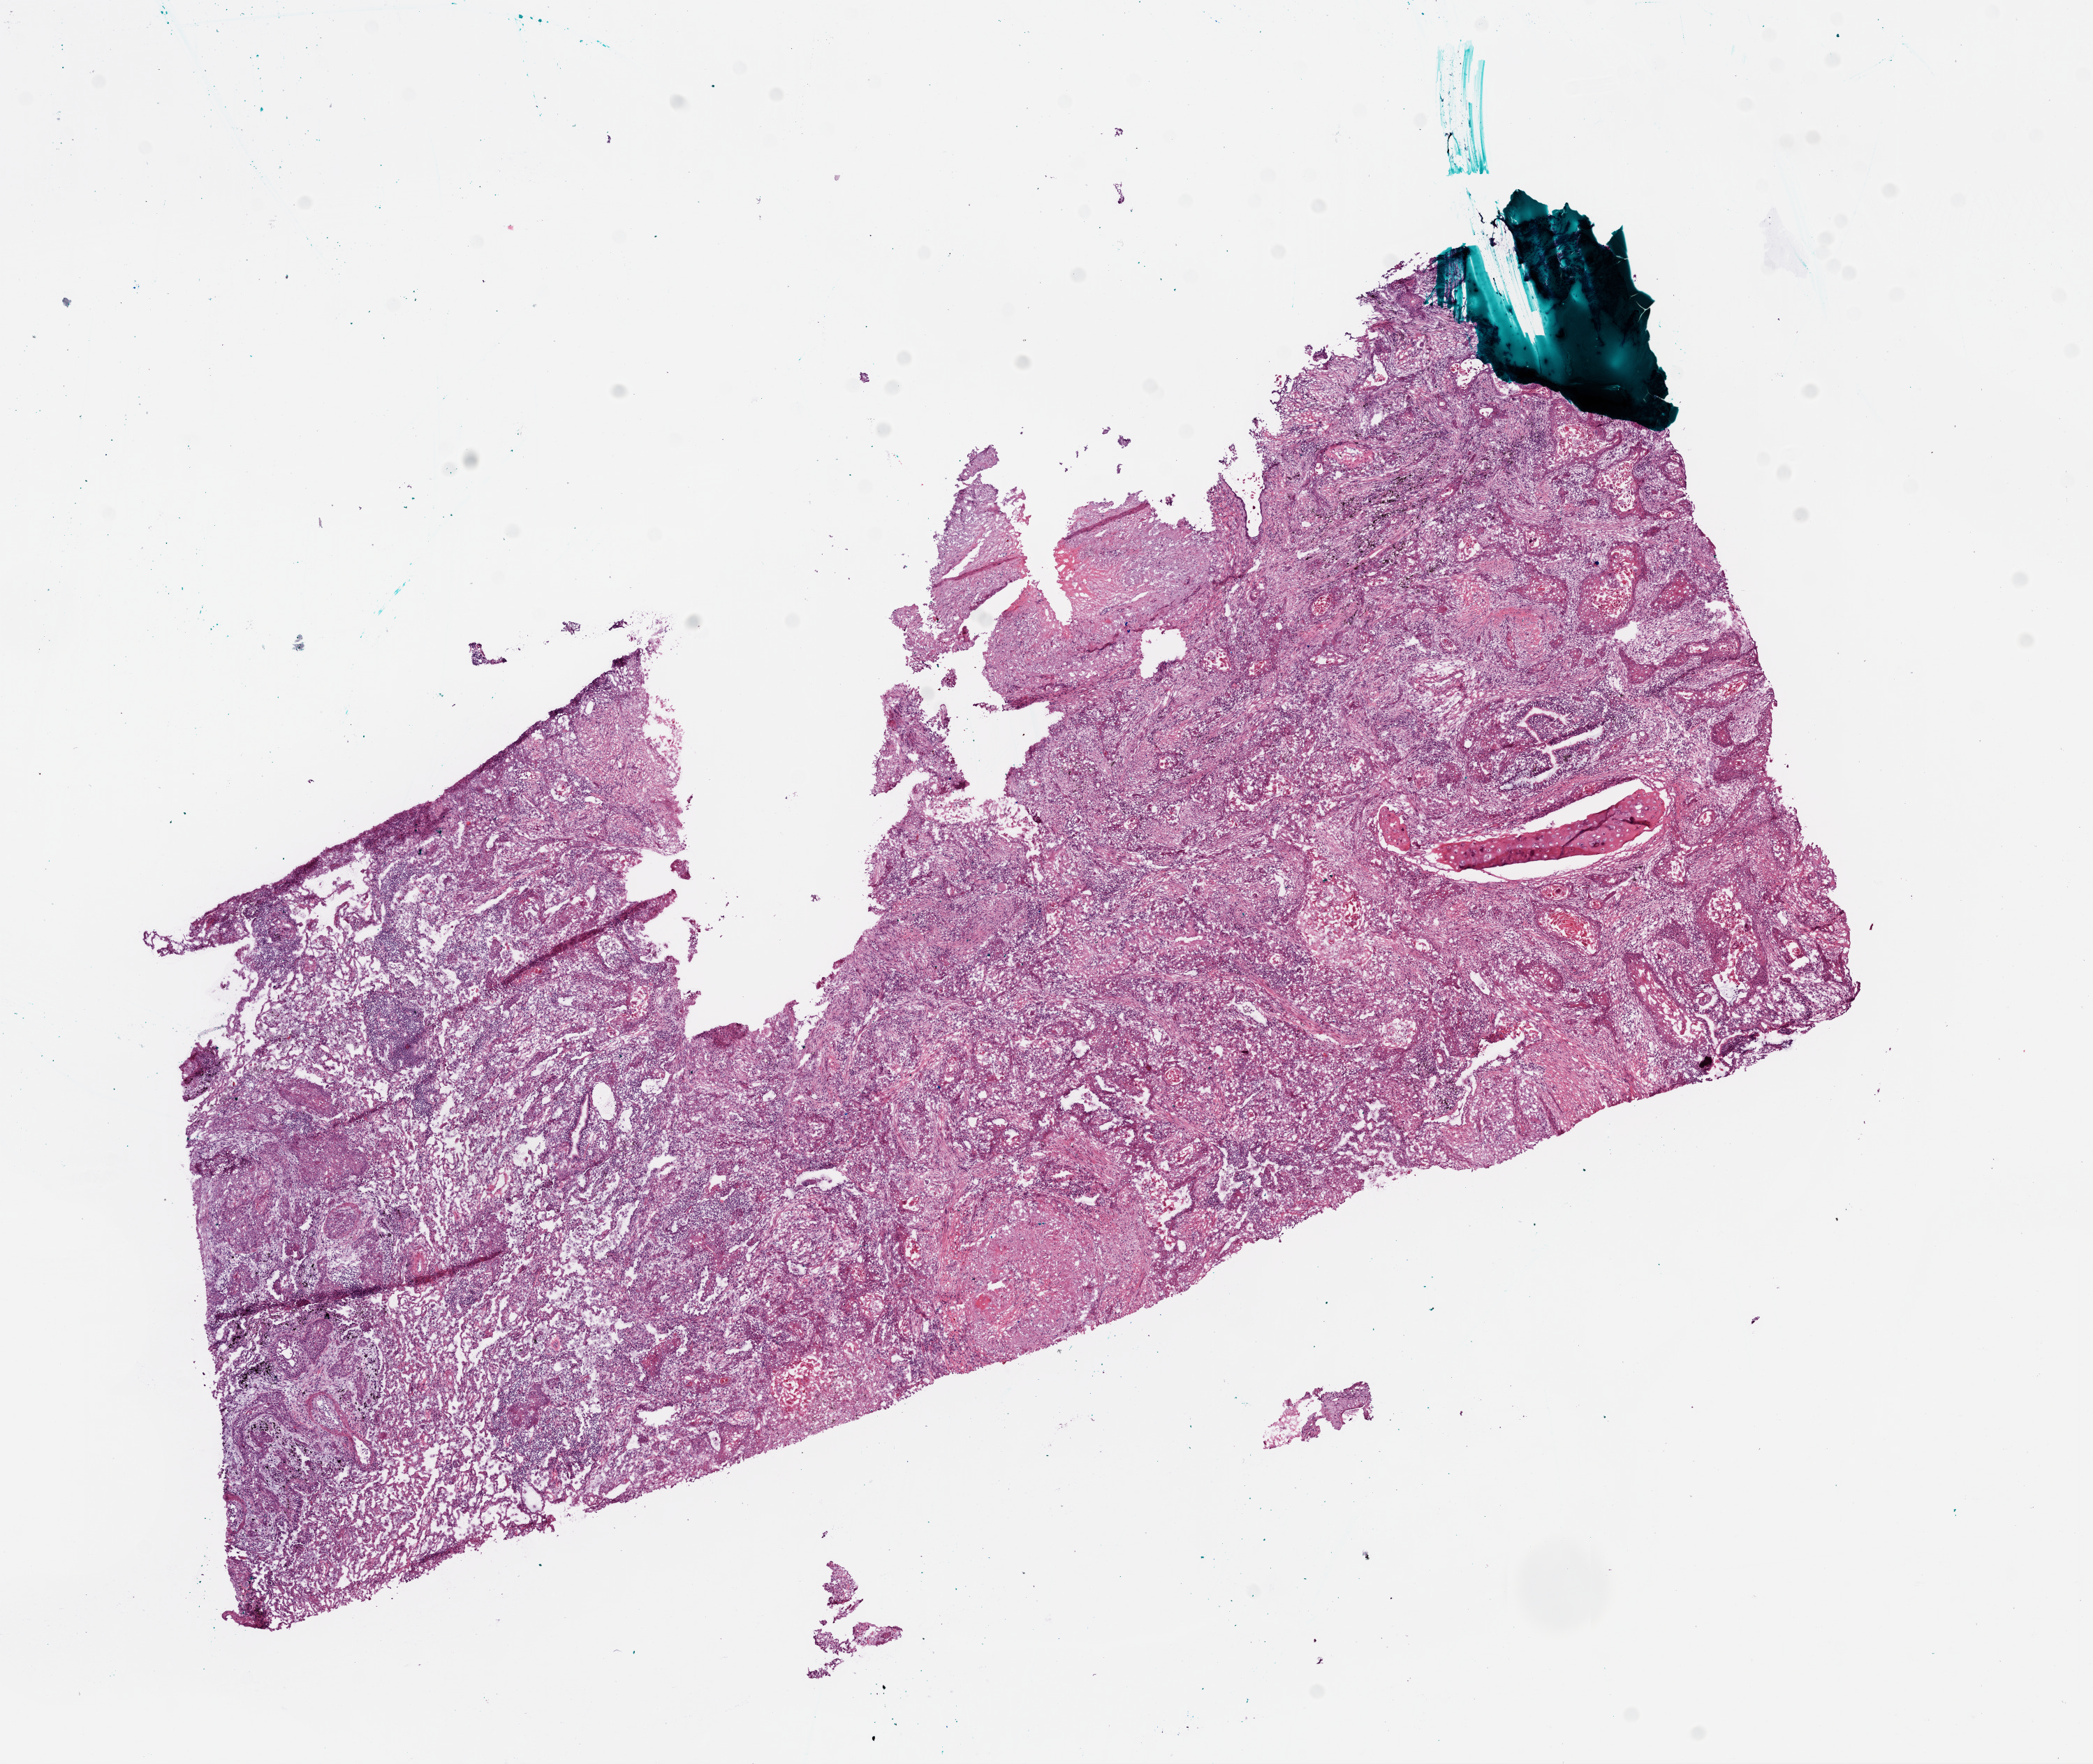
Hematoxylin and eosin (H&E) stained whole-slide image, shown as a low-resolution overview of the whole scanned area (about 12.1 x 10.2 mm, acquisition: 20x scan). Frozen section from the bottom of the tissue portion. Primary tumour sample from the lung. Patient: male, age at initial diagnosis 76 years. Slide review estimates, as recorded: tumour nuclei 60%, necrosis 5%.
AJCC pathologic stage: IB. Diagnosis: Squamous cell carcinoma, NOS.